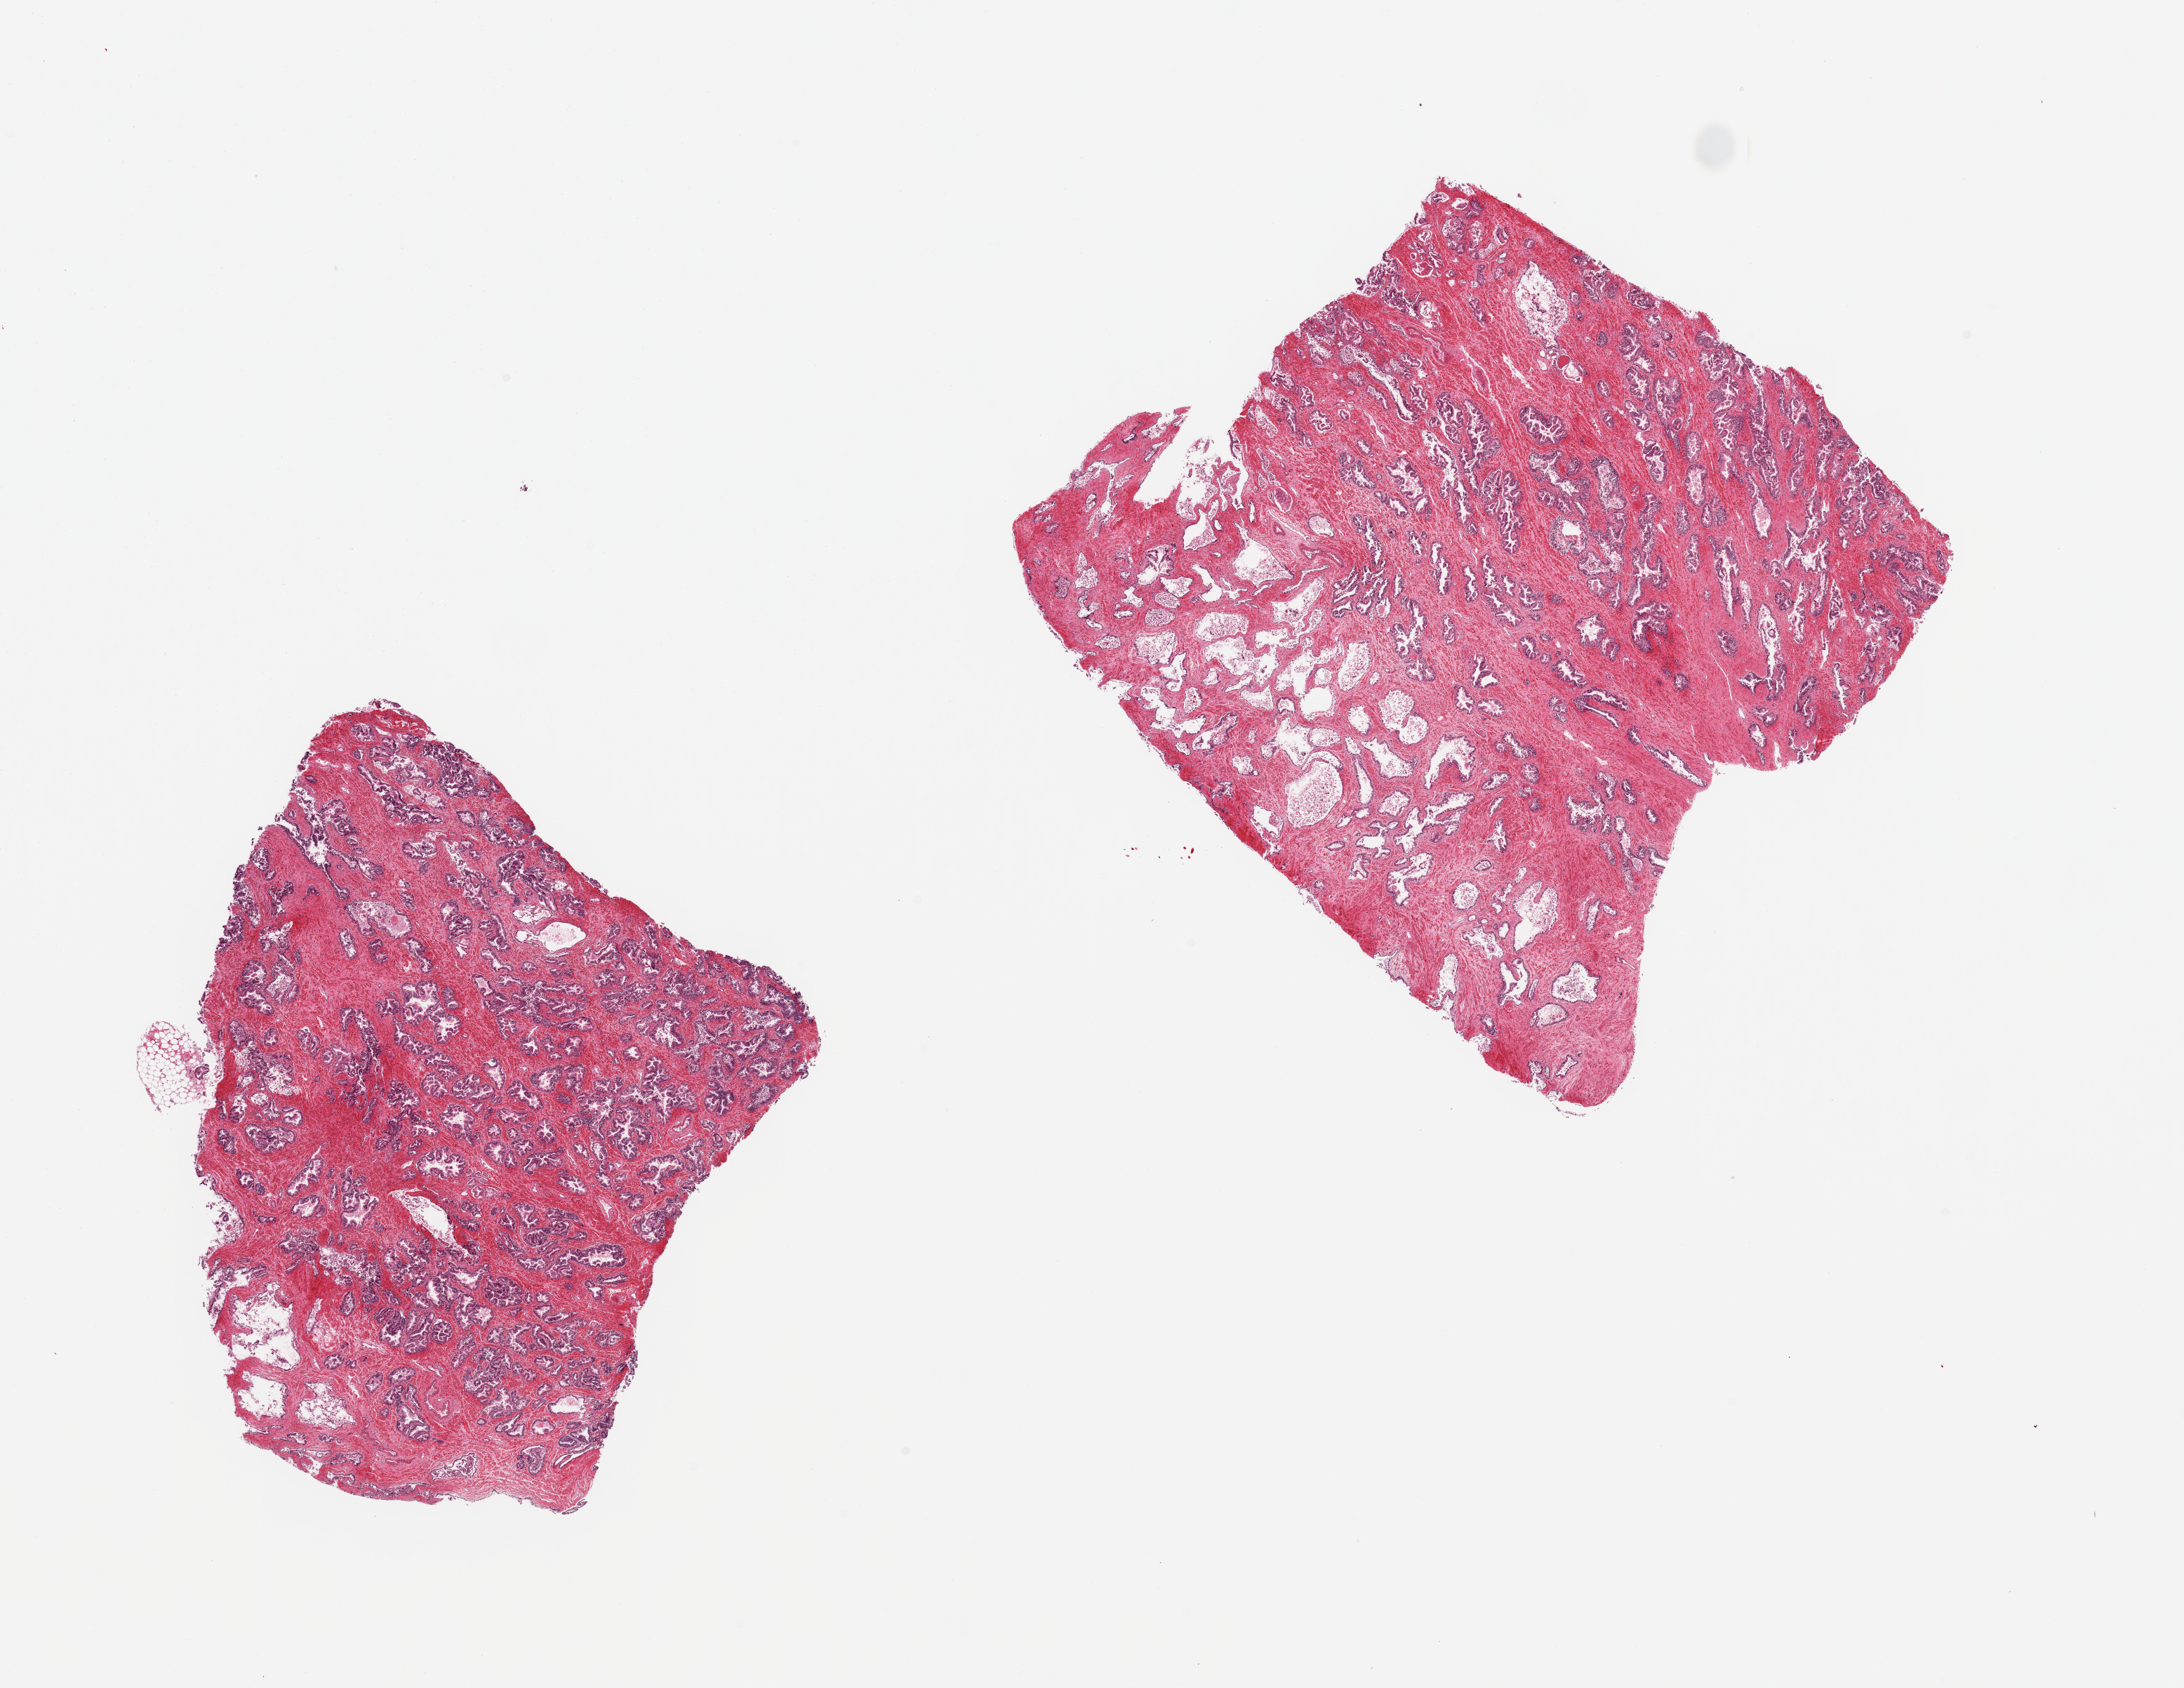
Digitized hematoxylin and eosin (H&E)-stained section, whole scanned area (about 24.6 x 19.0 mm, from a 20x scan) shown as a low-resolution overview. PAXgene-fixed, paraffin-embedded tissue. Sampled site (target tissue): prostate. Tissue donor sample. Donor: male.
Review note (as recorded): 2 pieces, galndular hyperplasia.